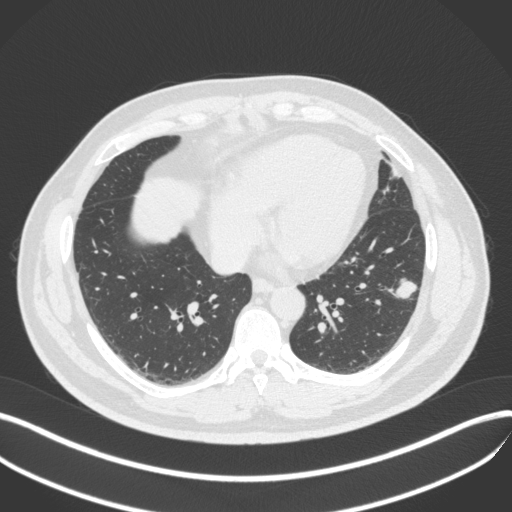
Chest CT, one axial slice; position 151 of 420 along the scan axis; 120 kVp; lung window (W 1500 / L -600 HU); 1 mm slice thickness; 512 × 512 image matrix. Male patient, age 39 years. Case-level facts recorded for this patient, not image findings: clinical TNM (as recorded): T2a N0 M0; histopathological grade: G2-3.
Structures marked on this image (rectangle marked by the reading radiologist):
- lung tumour (recorded histology: adenocarcinoma): bounding box <389,271,419,304> (left, top, right, bottom; pixels)